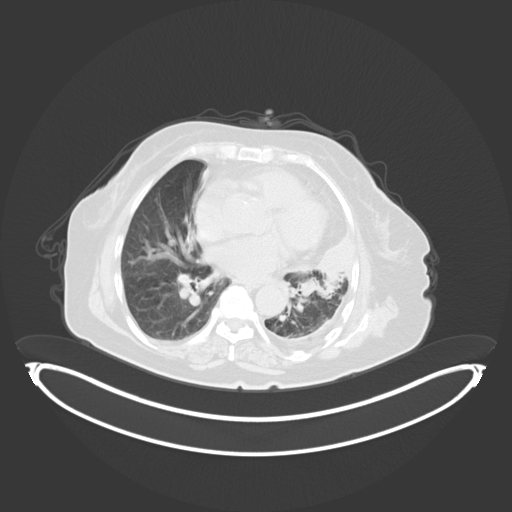
Chest CT, one axial slice. Slice 191 of 284 in the series (ordered by position). Reconstruction kernel B30f. 120 kVp. Lung window (W 1500 / L -600 HU). 3 mm slice thickness. 512 × 512 image matrix, field of view 500 × 500 mm. Female patient, age 75 years. From the clinical record (not read from this slice): clinical TNM (as recorded): T3 N3 M1.
Annotated regions visible in this slice (rectangle marked by the reading radiologist):
- lung tumour (recorded histology: adenocarcinoma): box from (x=302, y=233) to (x=359, y=293) px